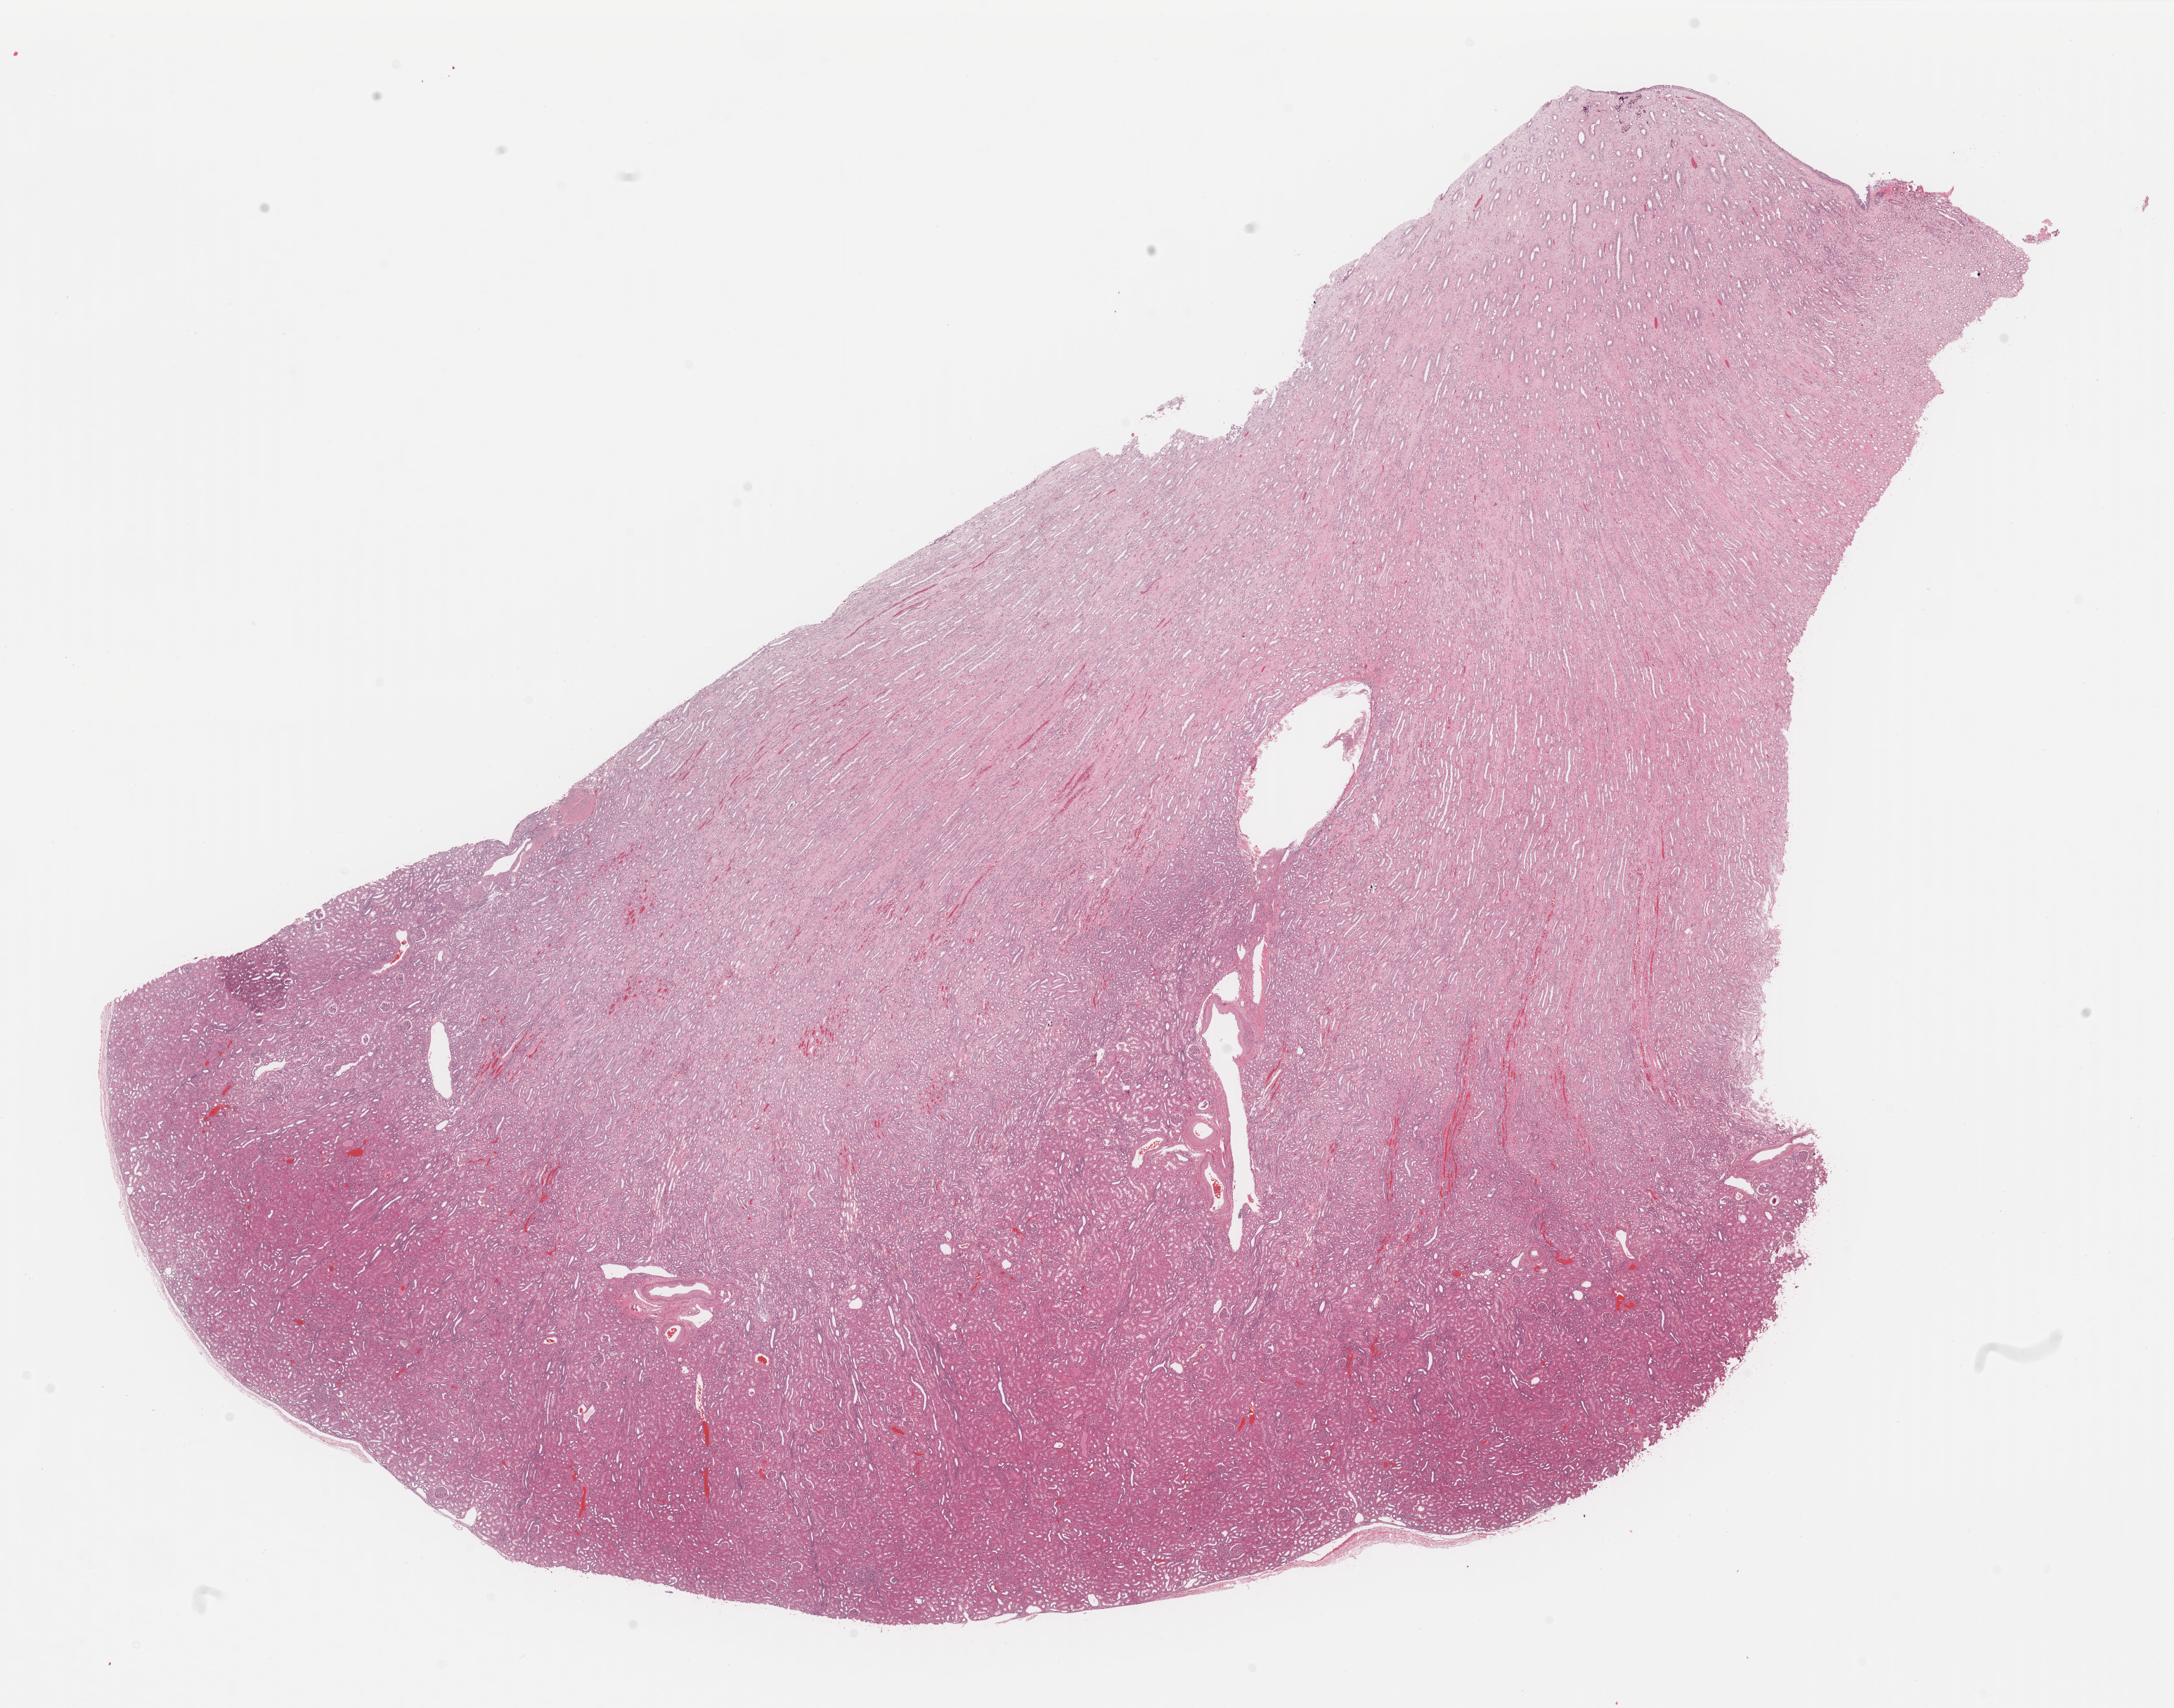
H&E whole-slide image — a low-resolution overview of the entire scanned area, about 24.5 x 19.2 mm. Formalin-fixed paraffin-embedded (FFPE) diagnostic section. Kidney, solid tissue normal (non-tumour tissue) sample. Female patient; age at initial diagnosis 74 years. Slide review estimates, as recorded: tumour cells 0%, tumour nuclei 0%, normal cells 70%, stromal cells 30%, necrosis 0%. Inflammatory infiltration, as recorded: lymphocyte infiltration 3%, monocyte infiltration 1%, neutrophil infiltration 1%.
- this section: solid tissue normal sample (biorepository sample class)
- patient diagnosis: Renal cell carcinoma, chromophobe type